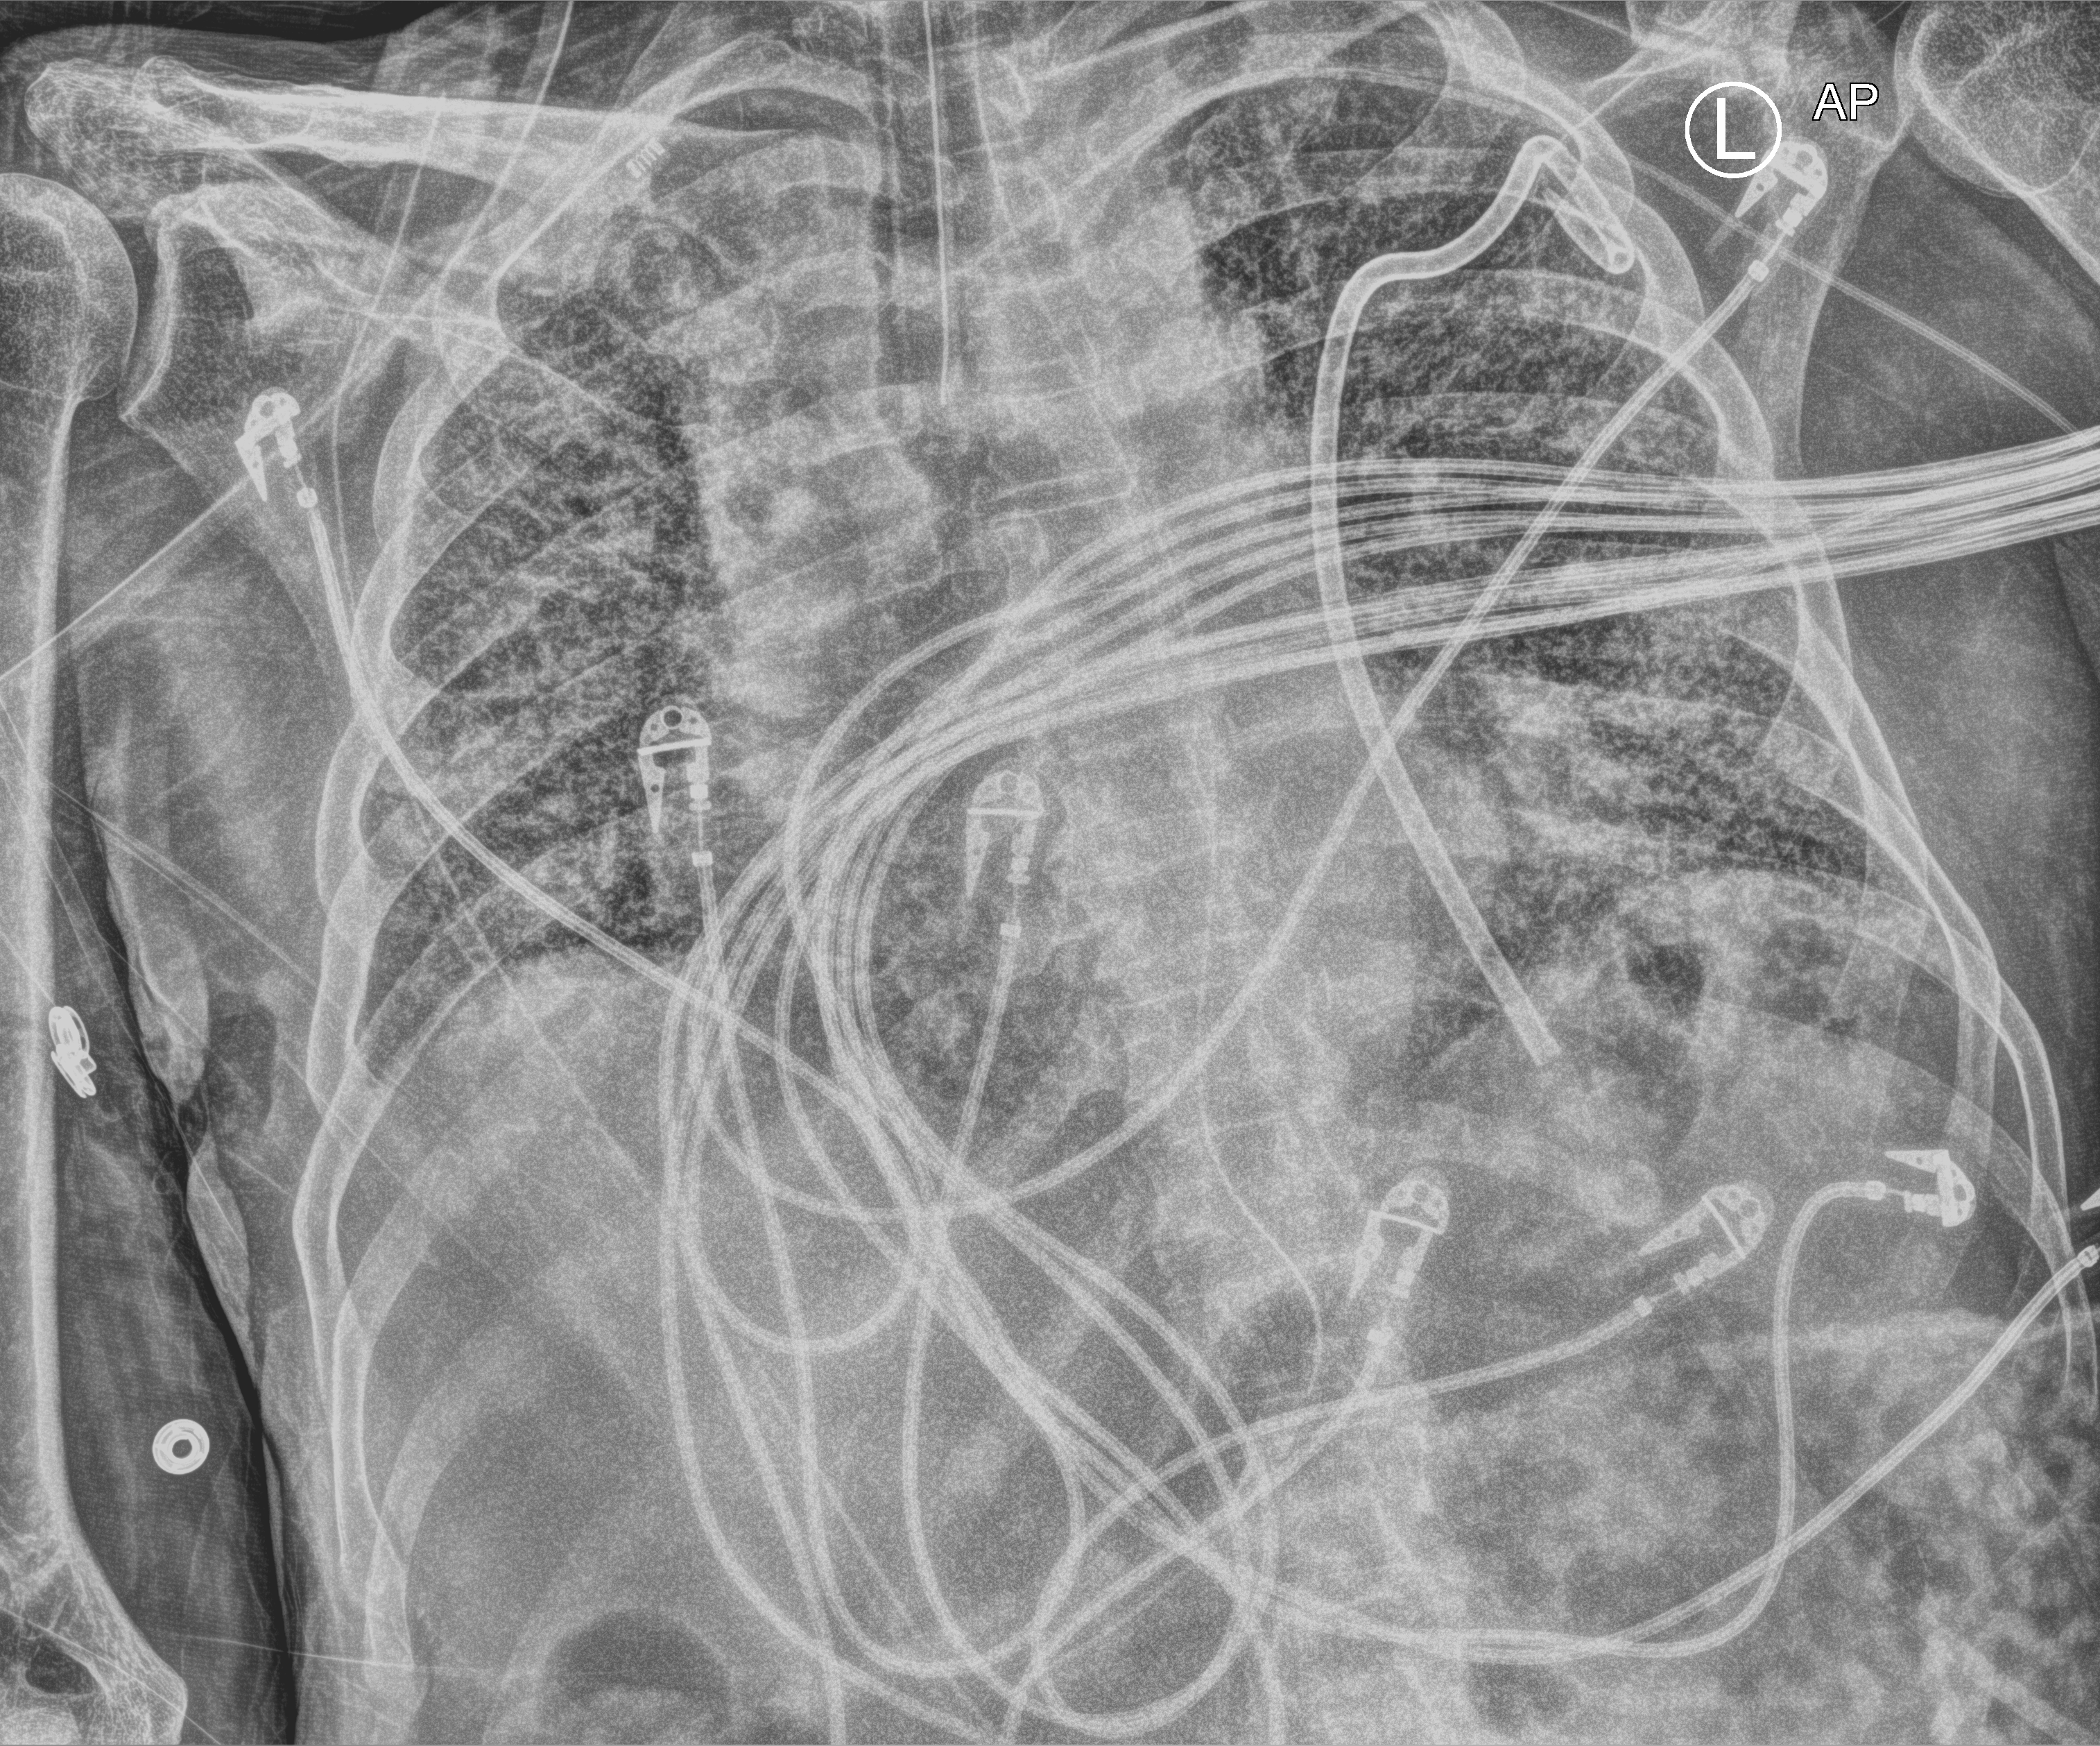
Portable chest radiograph. Patient hospitalised with COVID-19; male, aged 60–74 years.
From the hospital-stay record, not from the radiograph (when in the stay this image was taken is not recorded):
- admitted to intensive care during this hospital stay: yes
- mechanically ventilated during this hospital stay: yes
- length of hospital stay: 54 days